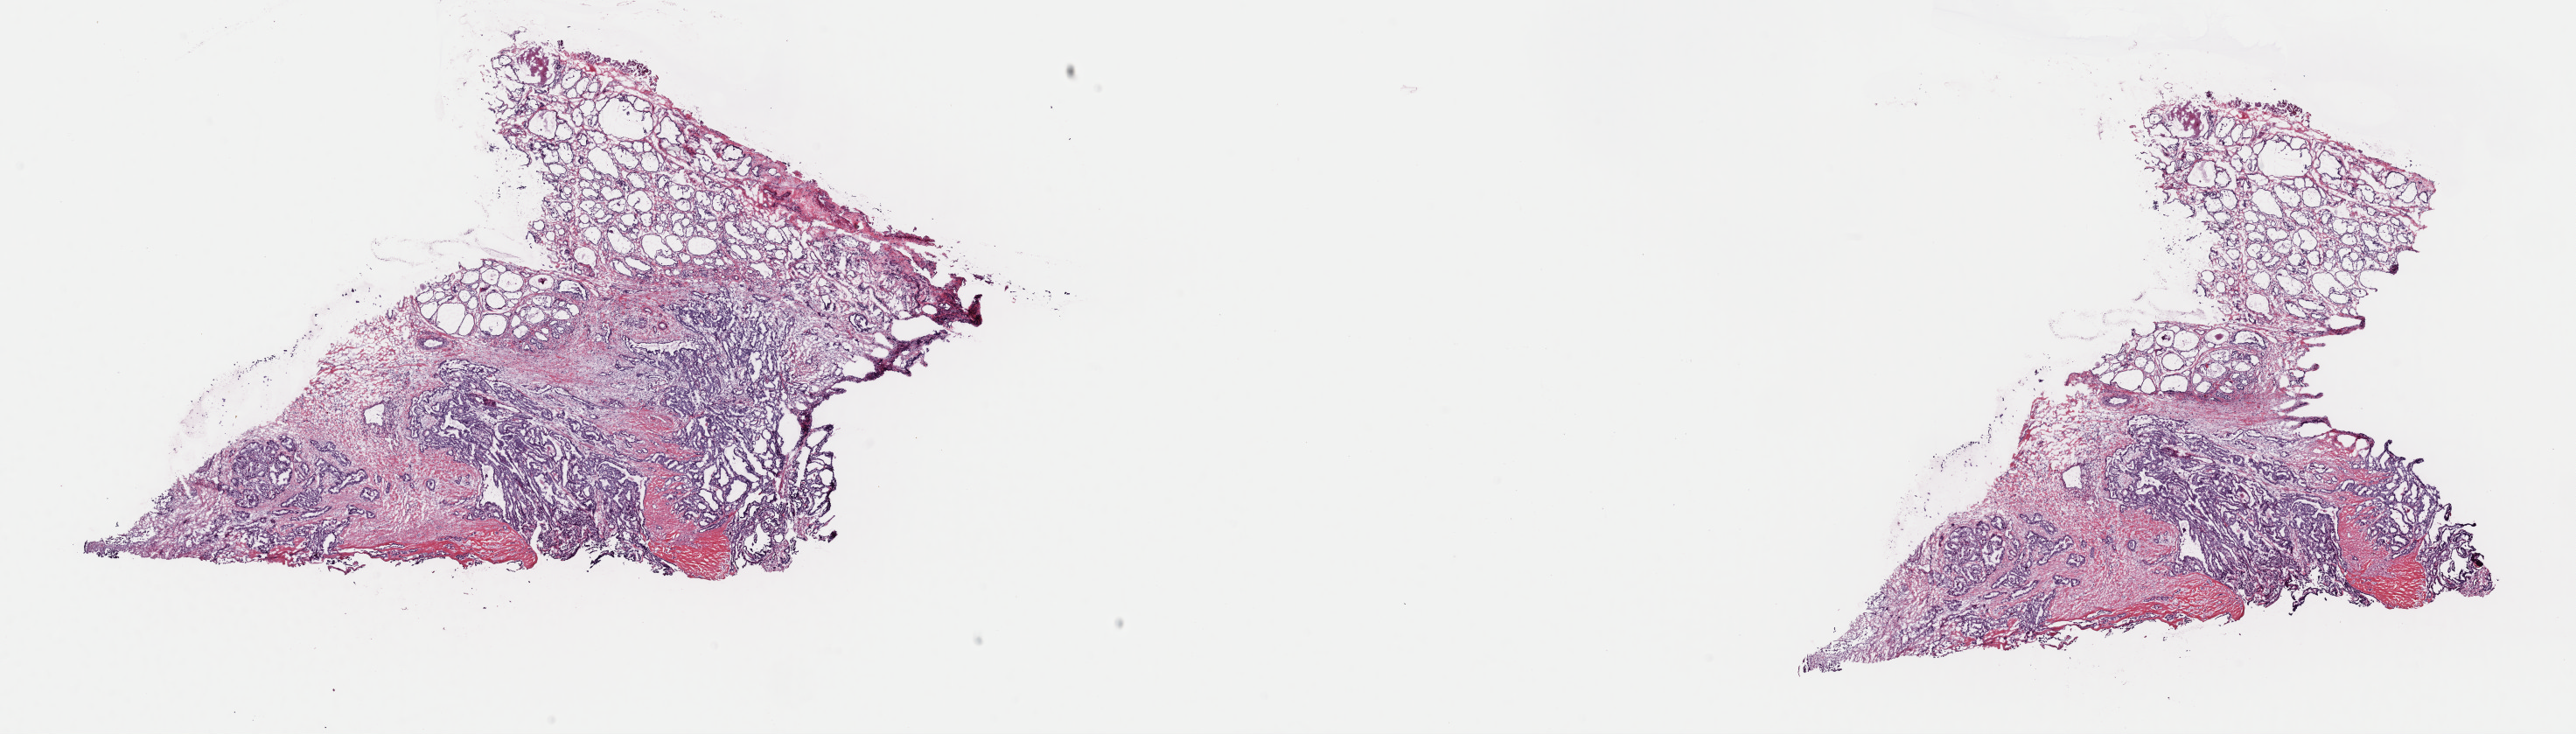
H&E whole-slide image, low-resolution overview of the scanned area, about 23.3 x 6.6 mm (from a 40x scan). Frozen section from the top of the tissue portion. Thyroid, primary tumour sample. Female patient; age at initial diagnosis 45 years. Pathologist review of this section (percent, as recorded): tumour cells 65%, tumour nuclei 65%.
Pathologic diagnosis: Papillary adenocarcinoma, NOS (thyroid gland).